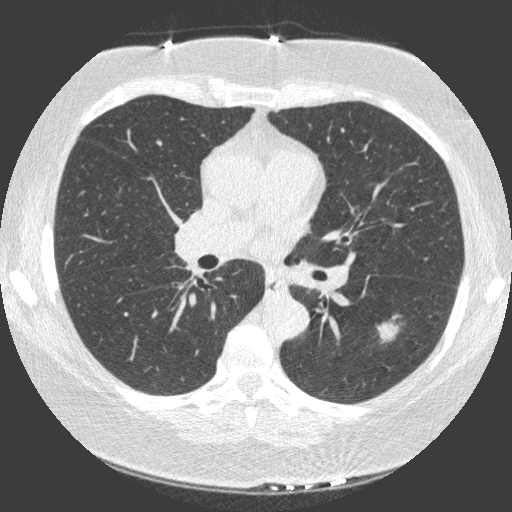
Low-dose screening chest CT, one axial slice. Lung window (W 1500 / L -600 HU). 1 mm slice thickness. 512 × 512 image matrix, field of view 330 × 330 mm.
Annotated regions visible in this slice (outlined manually by an expert reader):
- lesion 1 (tumor, lower lobe of left lung): bounding box <377,323,398,341> (left, top, right, bottom; pixels)